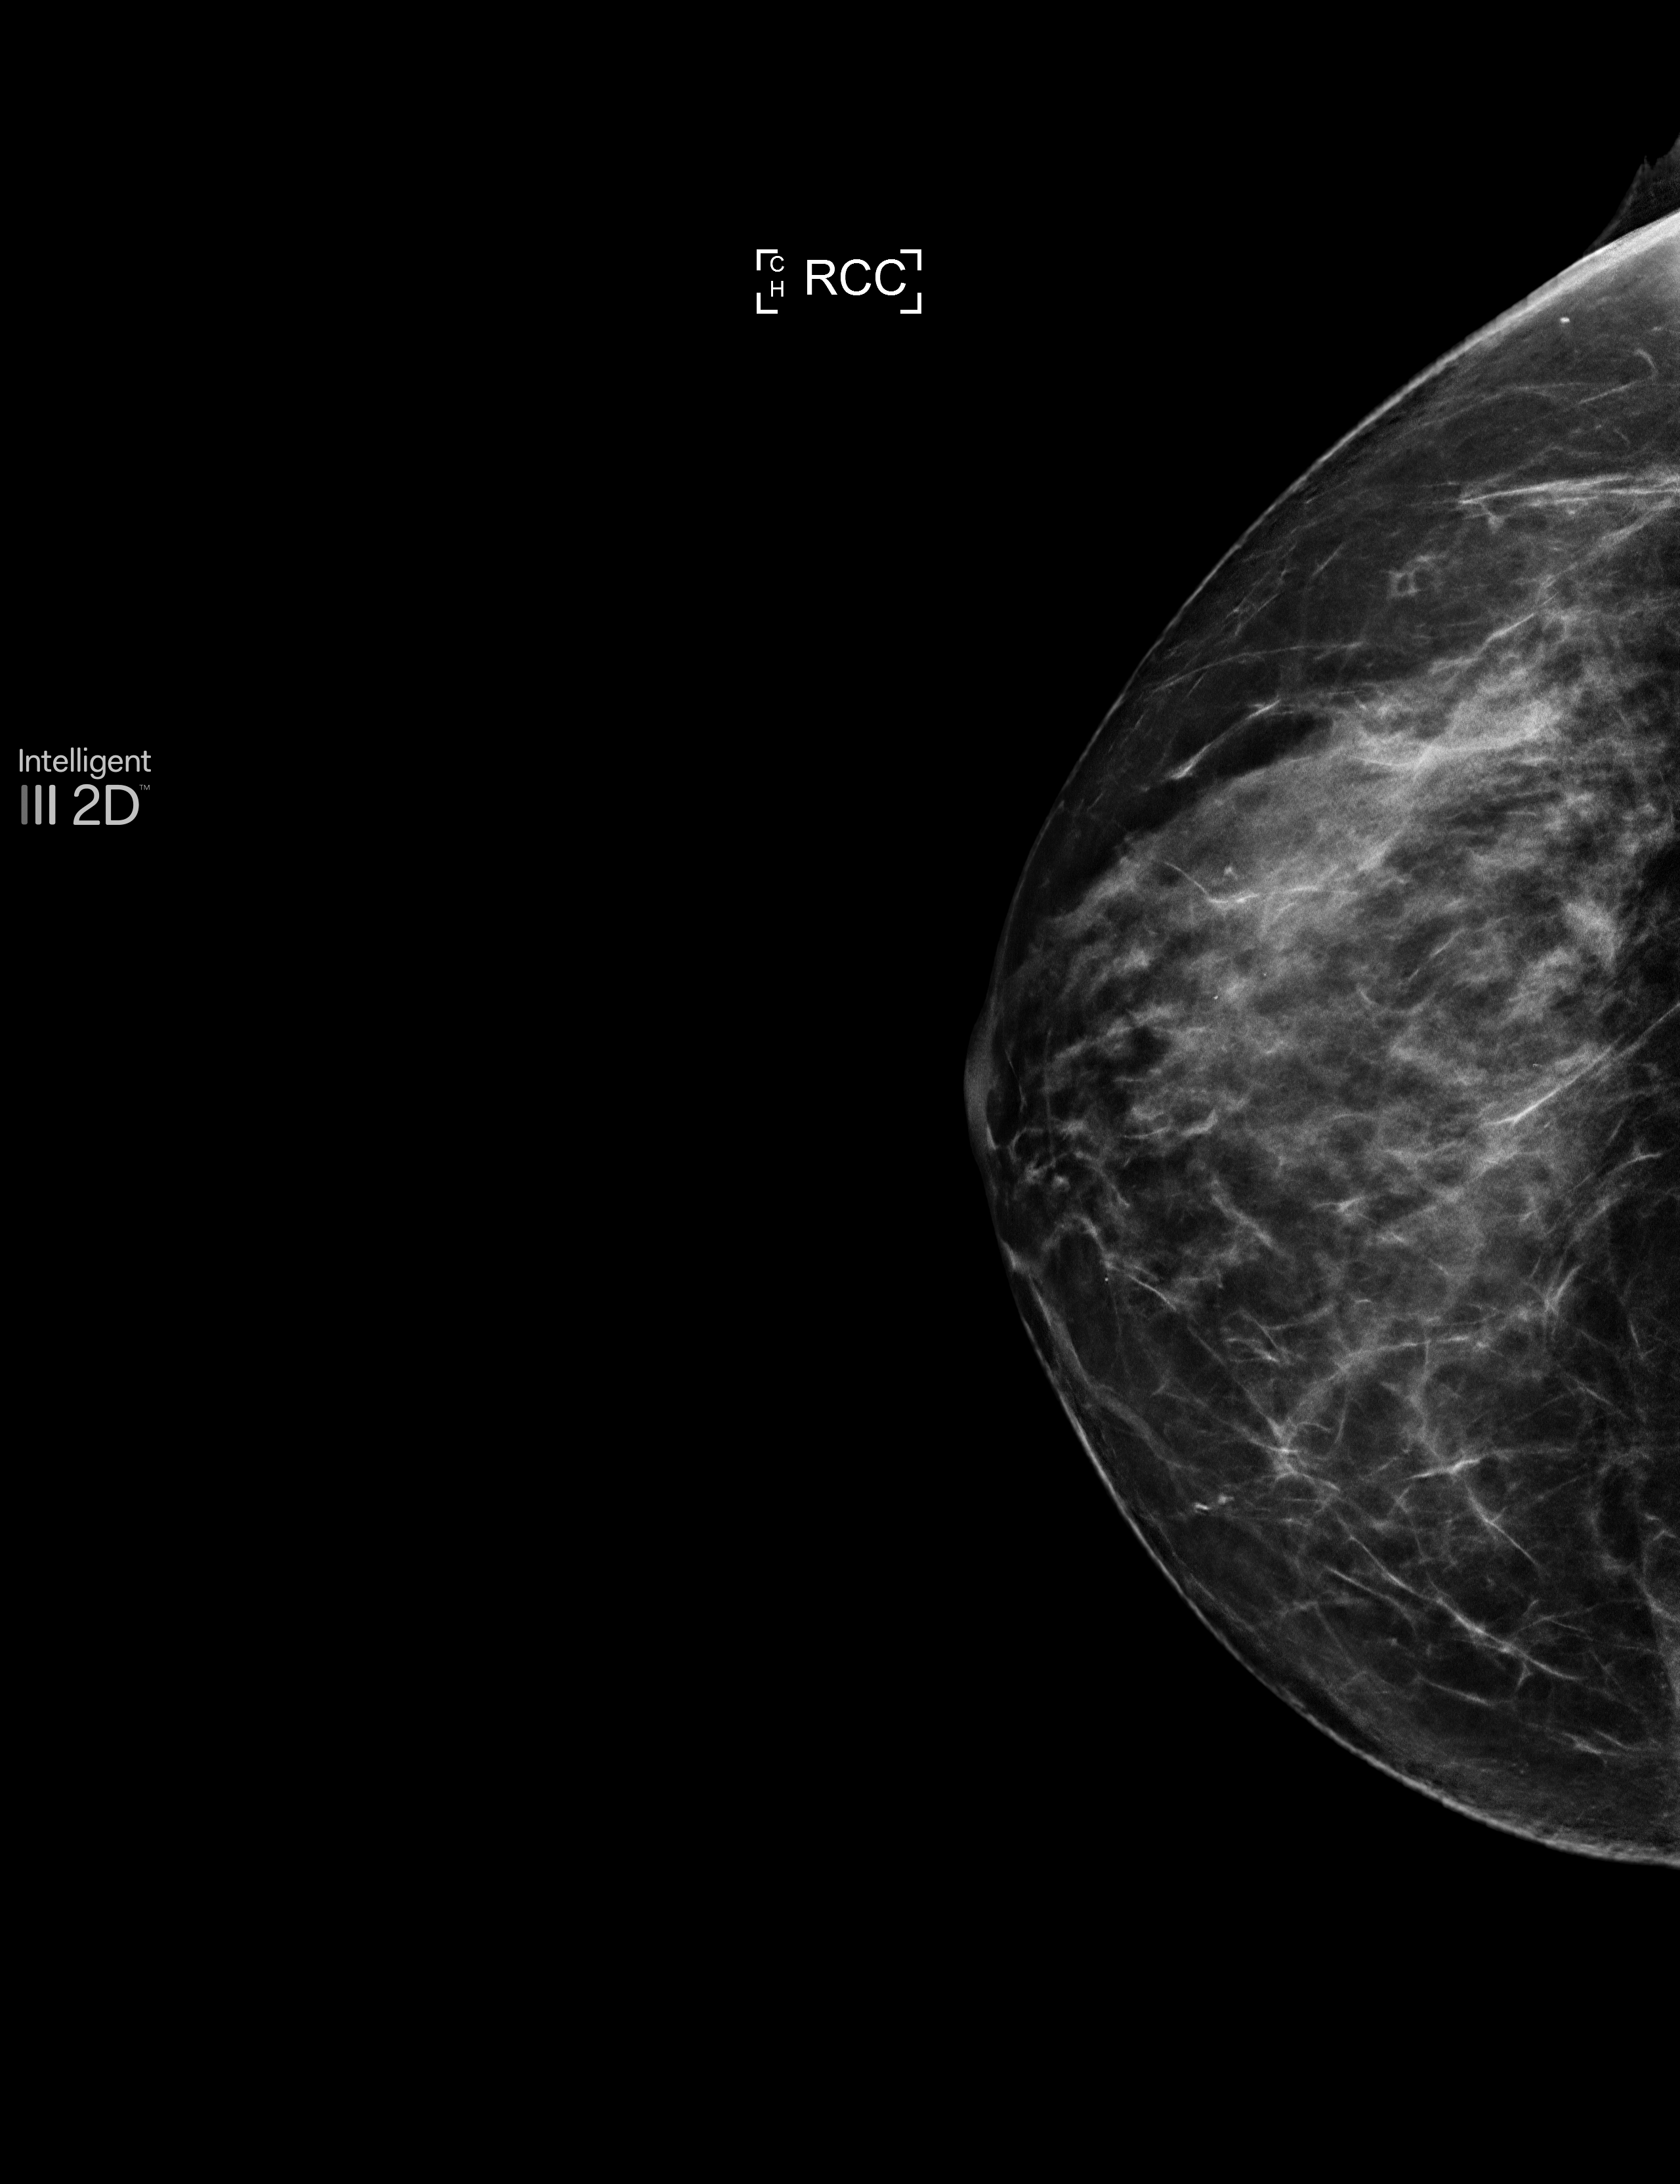
Annual screening mammography examination; compressed breast thickness 57 mm; system: Selenia Dimensions. Female patient, age 60 years.
Image type: synthesized 2-D view from tomosynthesis. Breast: right. Projection: craniocaudal (CC) view.